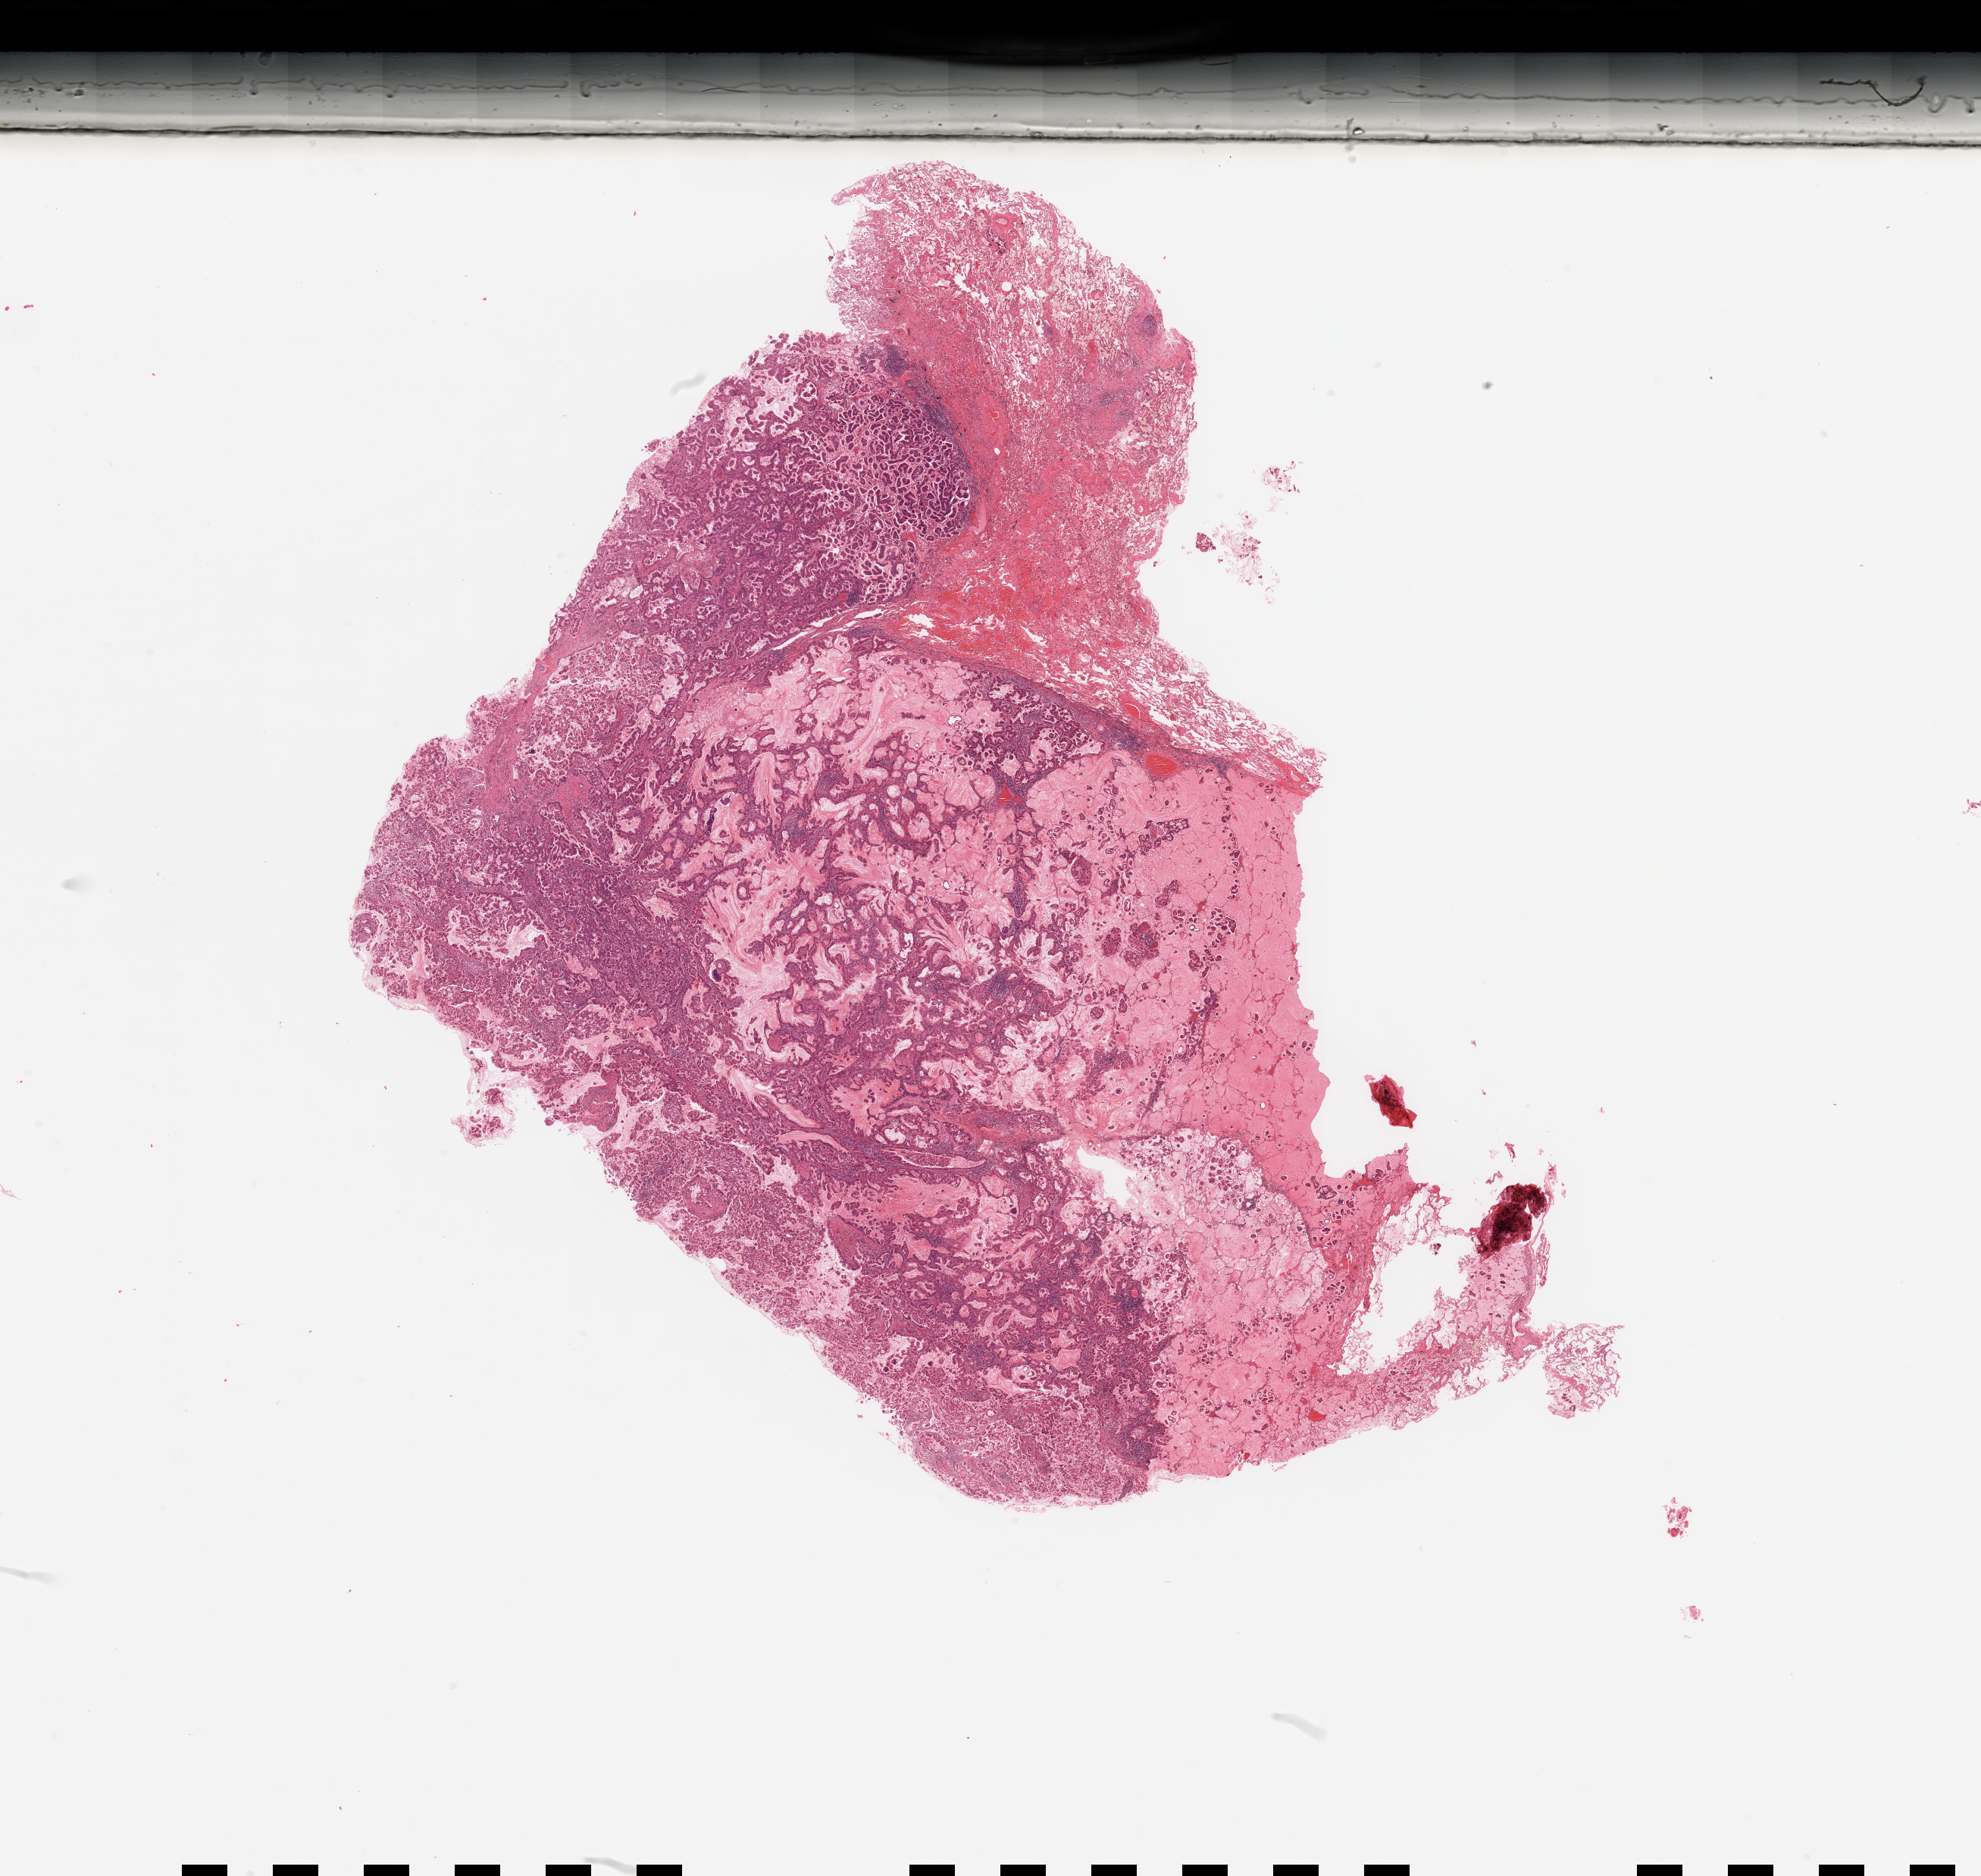
Digitized H&E tissue section (whole slide) — shown as a low-resolution overview of the whole scanned area (about 20.7 x 19.6 mm); tumour tissue sample, lung. Patient: female, age 52 years. Histologic grade: G2 (moderately differentiated).
Diagnosis: Adenocarcinoma, NOS. Primary tumour site (as recorded): left lower lobe. AJCC pathologic stage: IIA.